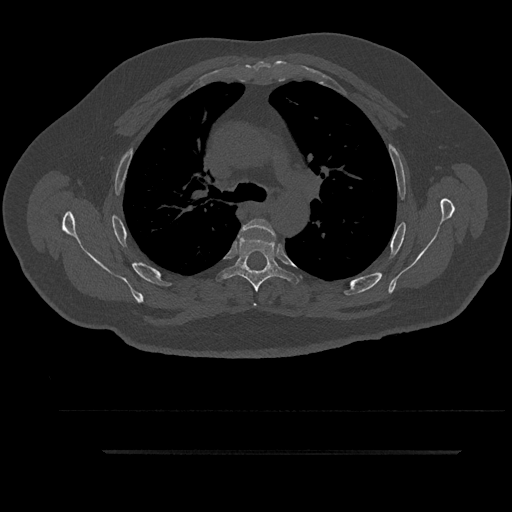
CT including the spine, one axial slice; slice 636 of 797 in the series (ordered by position); reconstruction kernel Br40s/3; 120 kVp; bone window (W 1800 / L 400 HU); 0.5 mm slice thickness; 512 × 512 image matrix, field of view 432 × 432 mm. Patient: male, 63 years. Case-level facts recorded for this patient, not image findings: primary cancer: renal; vertebrae with lytic lesions (as recorded): T8.
Structures marked on this image (semi-automatic segmentation, software-assisted and operator-edited):
- T4 vertebra: bounding box [x1, y1, x2, y2] px = [238, 219, 274, 306]
- T5 vertebra: [216, 229, 299, 292]